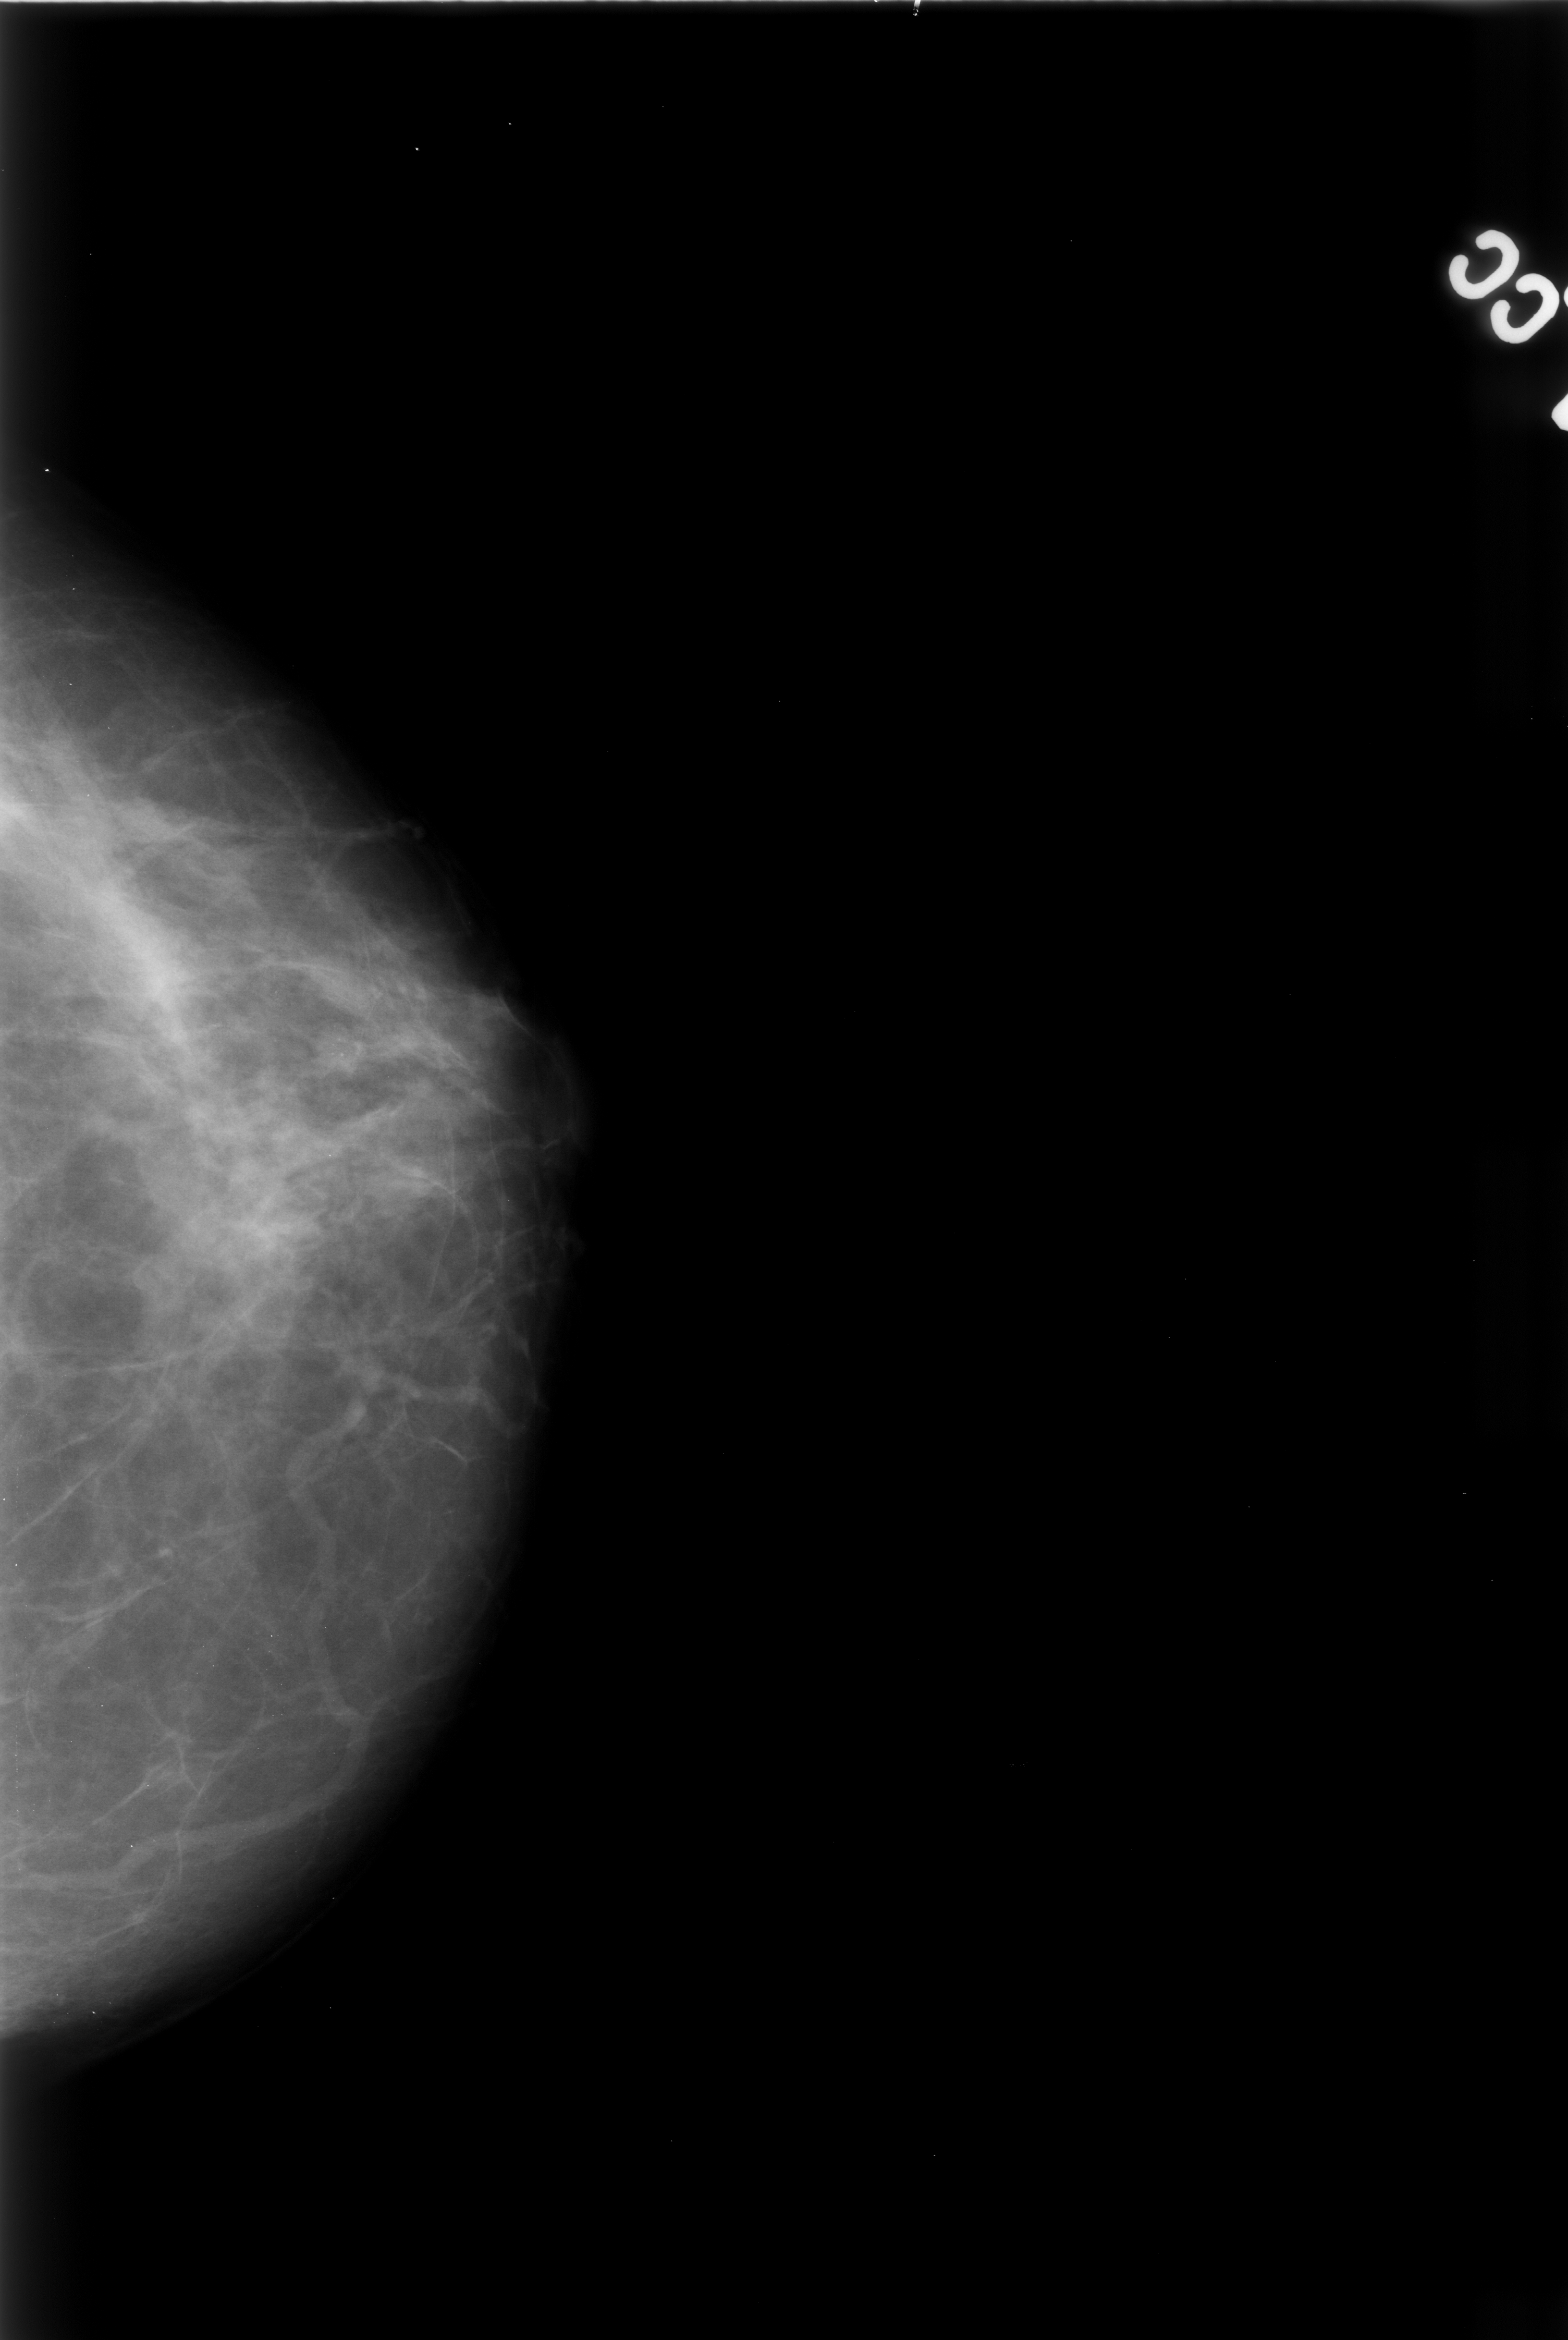
Digitized screen-film mammogram. Left breast. Craniocaudal (CC) view. Breast composition: scattered fibroglandular densities (BI-RADS density category 2 of 4). 1568 × 2340 image matrix.
Marked abnormalities (boxes around the expert regions of interest):
- calcifications, morphology punctate, distribution clustered; BI-RADS assessment category 4; subtlety rating 3 on a 1 (subtle) to 5 (obvious) scale; pathology (as recorded): benign: box from (x=283, y=1005) to (x=397, y=1098) px